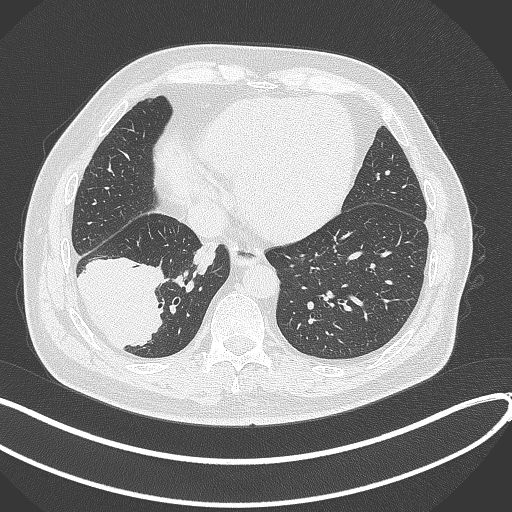
Chest CT, one axial slice. Position 102 of 360 along the scan axis. Reconstruction kernel B70f. Lung window (W 1500 / L -600 HU). 1 mm slice thickness. 512 × 512 image matrix. Male patient, age 59 years.
Structures marked on this image (rectangle marked by the reading radiologist):
- lung tumour (recorded histology: adenocarcinoma): bounding box [x1, y1, x2, y2] px = [73, 253, 170, 351]